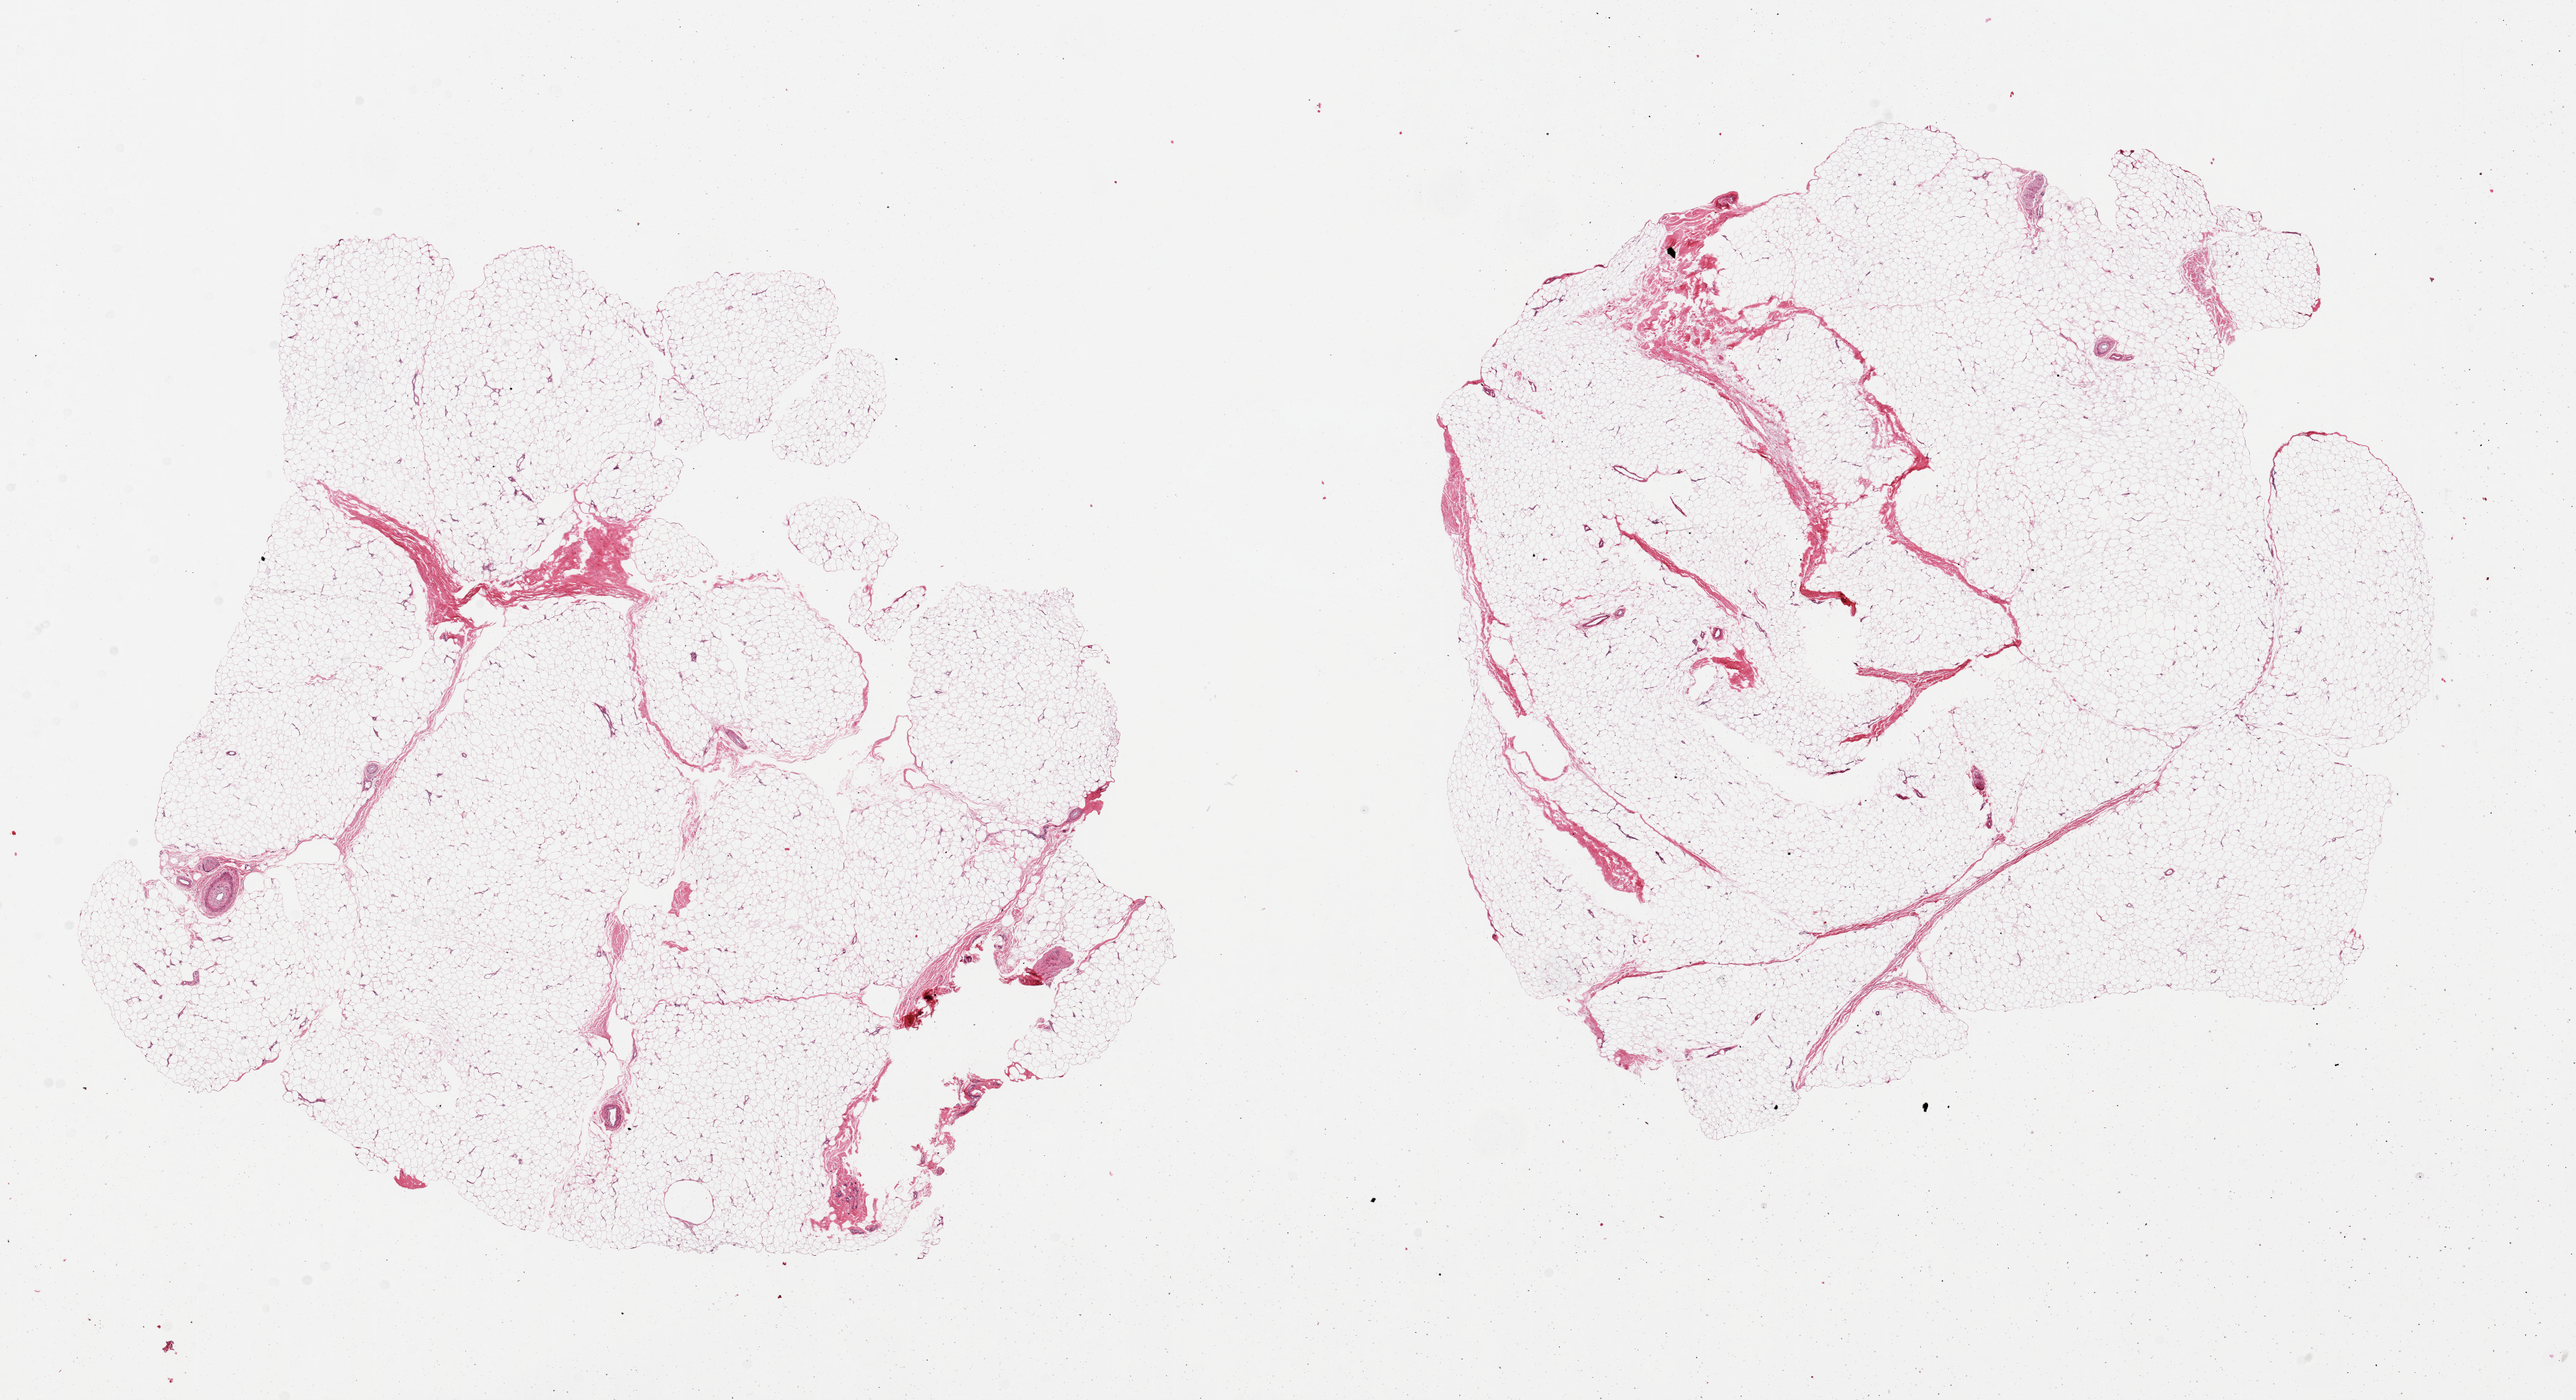
Haematoxylin and eosin whole-slide image — whole scanned area (about 28.5 x 15.5 mm, slide scanned at 20x) shown as a low-resolution overview, PAXgene-fixed paraffin-embedded (PFPE) section, target tissue: adipose tissue, tissue donor sample. Donor sex: female.
Reviewer comment on this tissue sample: 2 pieces; ~5-10% interstitial fascia/fibrous tissue.